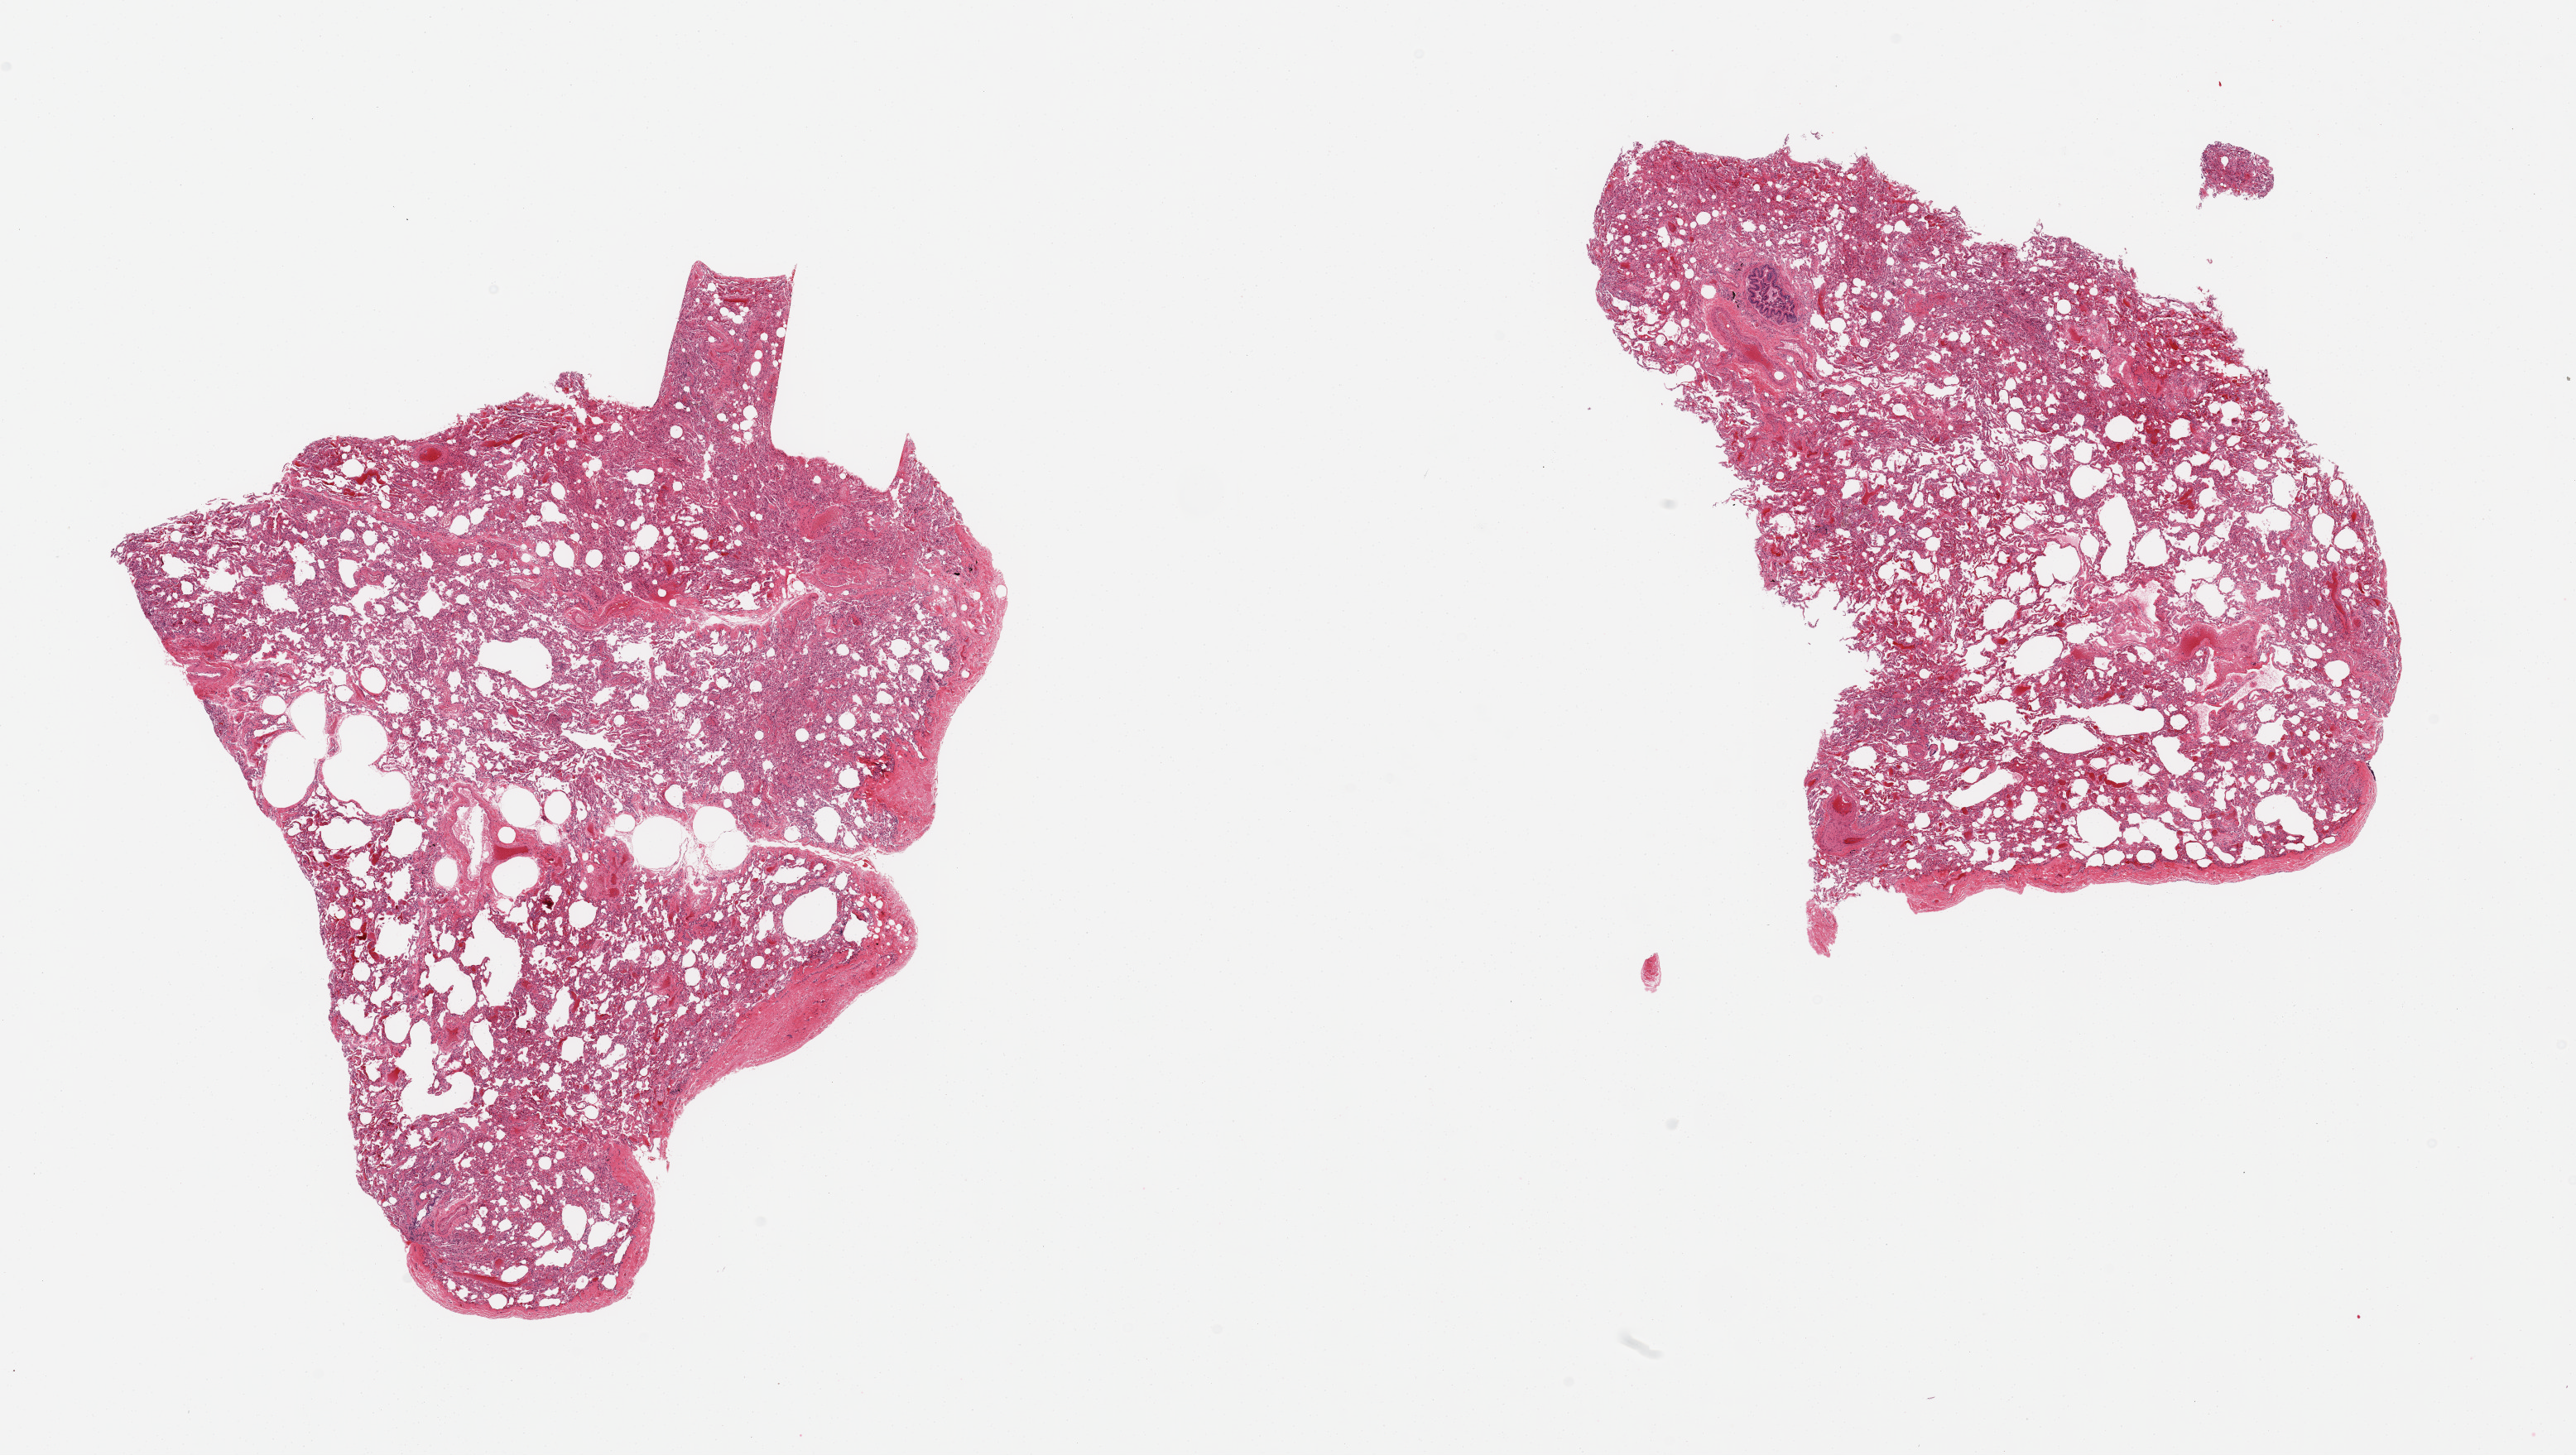
H&E whole-slide image — a low-resolution overview of the entire scanned area, about 24.6 x 13.9 mm (slide scanned at 20x). PAXgene-fixed paraffin-embedded (PFPE) section. Sampled site (target tissue): lung. Tissue donor sample. Donor sex: female.
Review note (as recorded): 2 pieces, moderate congestion, ? emphysematous changes.